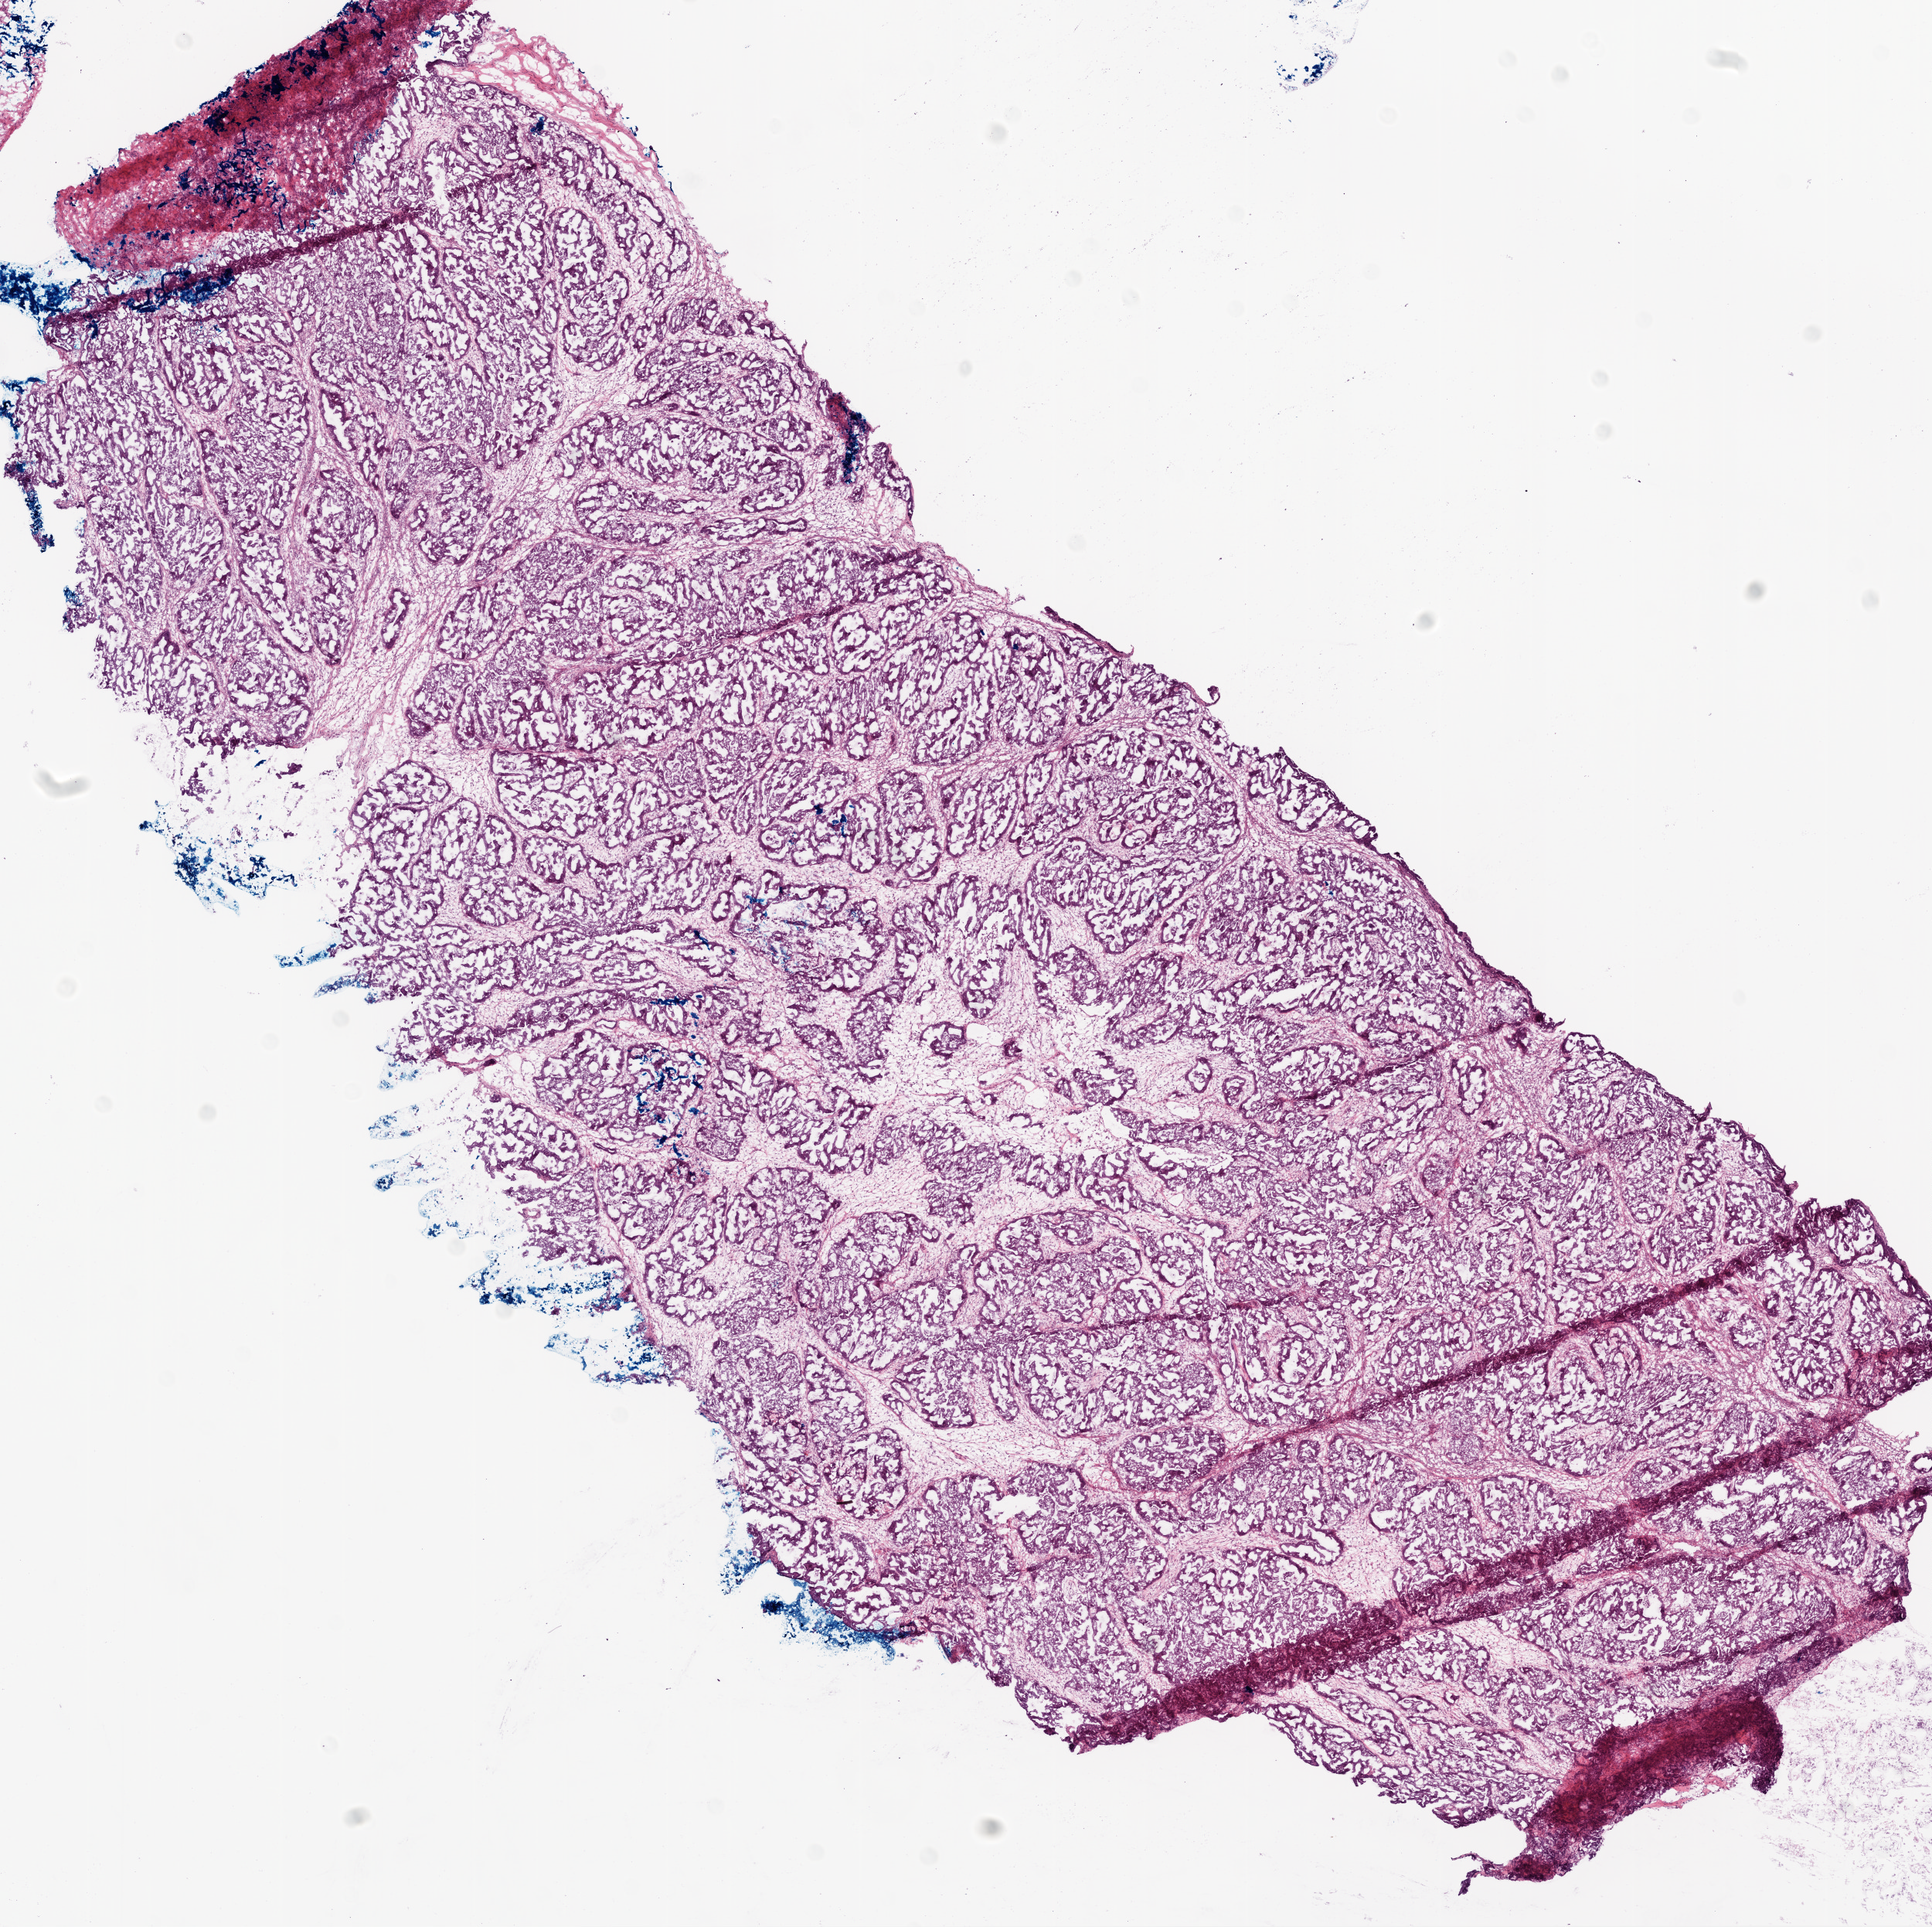
Digitized H&E tissue section (whole slide), shown as a low-resolution overview of the whole scanned area (about 10.0 x 10.0 mm, from a 20x scan). Frozen section. Ovary, primary tumour sample. Female patient; age at initial diagnosis 47 years.
Pathologic diagnosis: Serous cystadenocarcinoma, NOS.